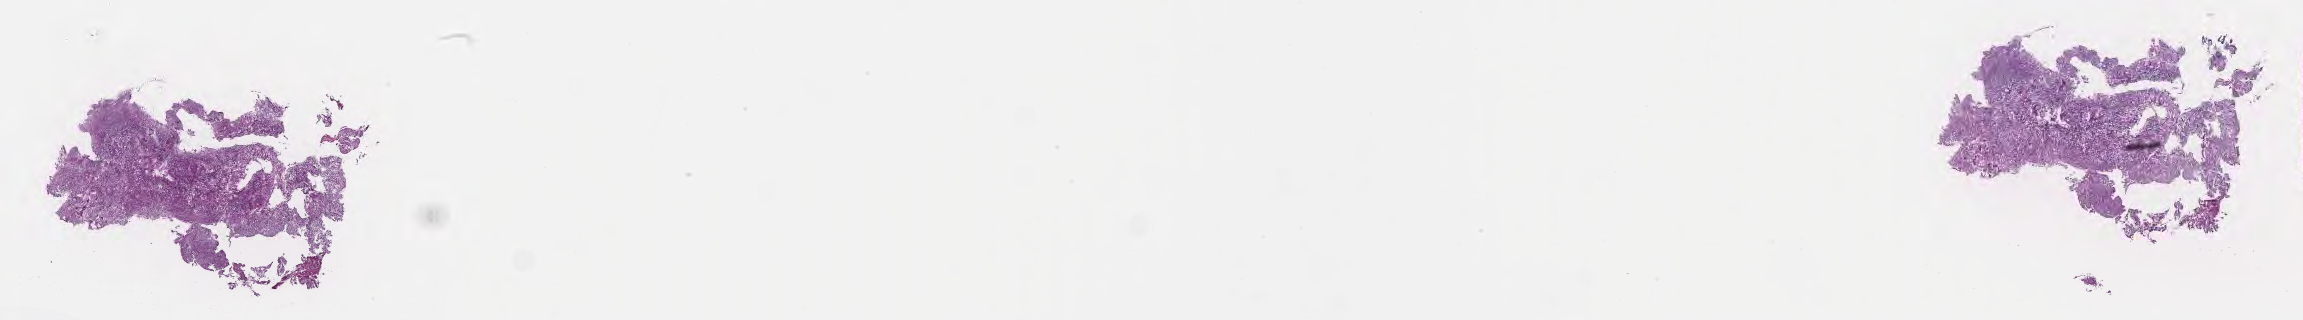
Haematoxylin and eosin whole-slide image of tumor tissue from the brain — whole scanned area (about 37.2 x 5.2 mm) shown as a low-resolution overview; frozen section. Male patient, age 377 days.
• recorded diagnosis: Ependymoma, NOS